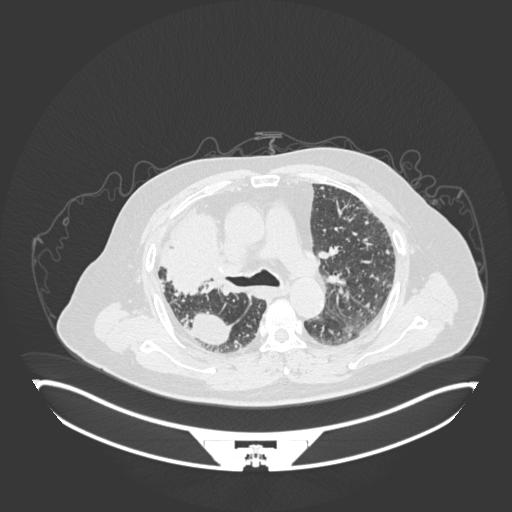
Chest CT, one axial slice; slice 117 of 201 in the series (ordered by position); reconstruction kernel B30f; 120 kVp; lung window (W 1500 / L -600 HU); 512 × 512 image matrix. Patient: male, 69 years. Case-level facts recorded for this patient, not image findings: clinical TNM (as recorded): T4 N3 M1.
Annotated regions visible in this slice (rectangle marked by the reading radiologist):
- lung tumour (recorded histology: adenocarcinoma): bounding box (x1, y1, x2, y2) in pixels: (157, 208, 243, 301)